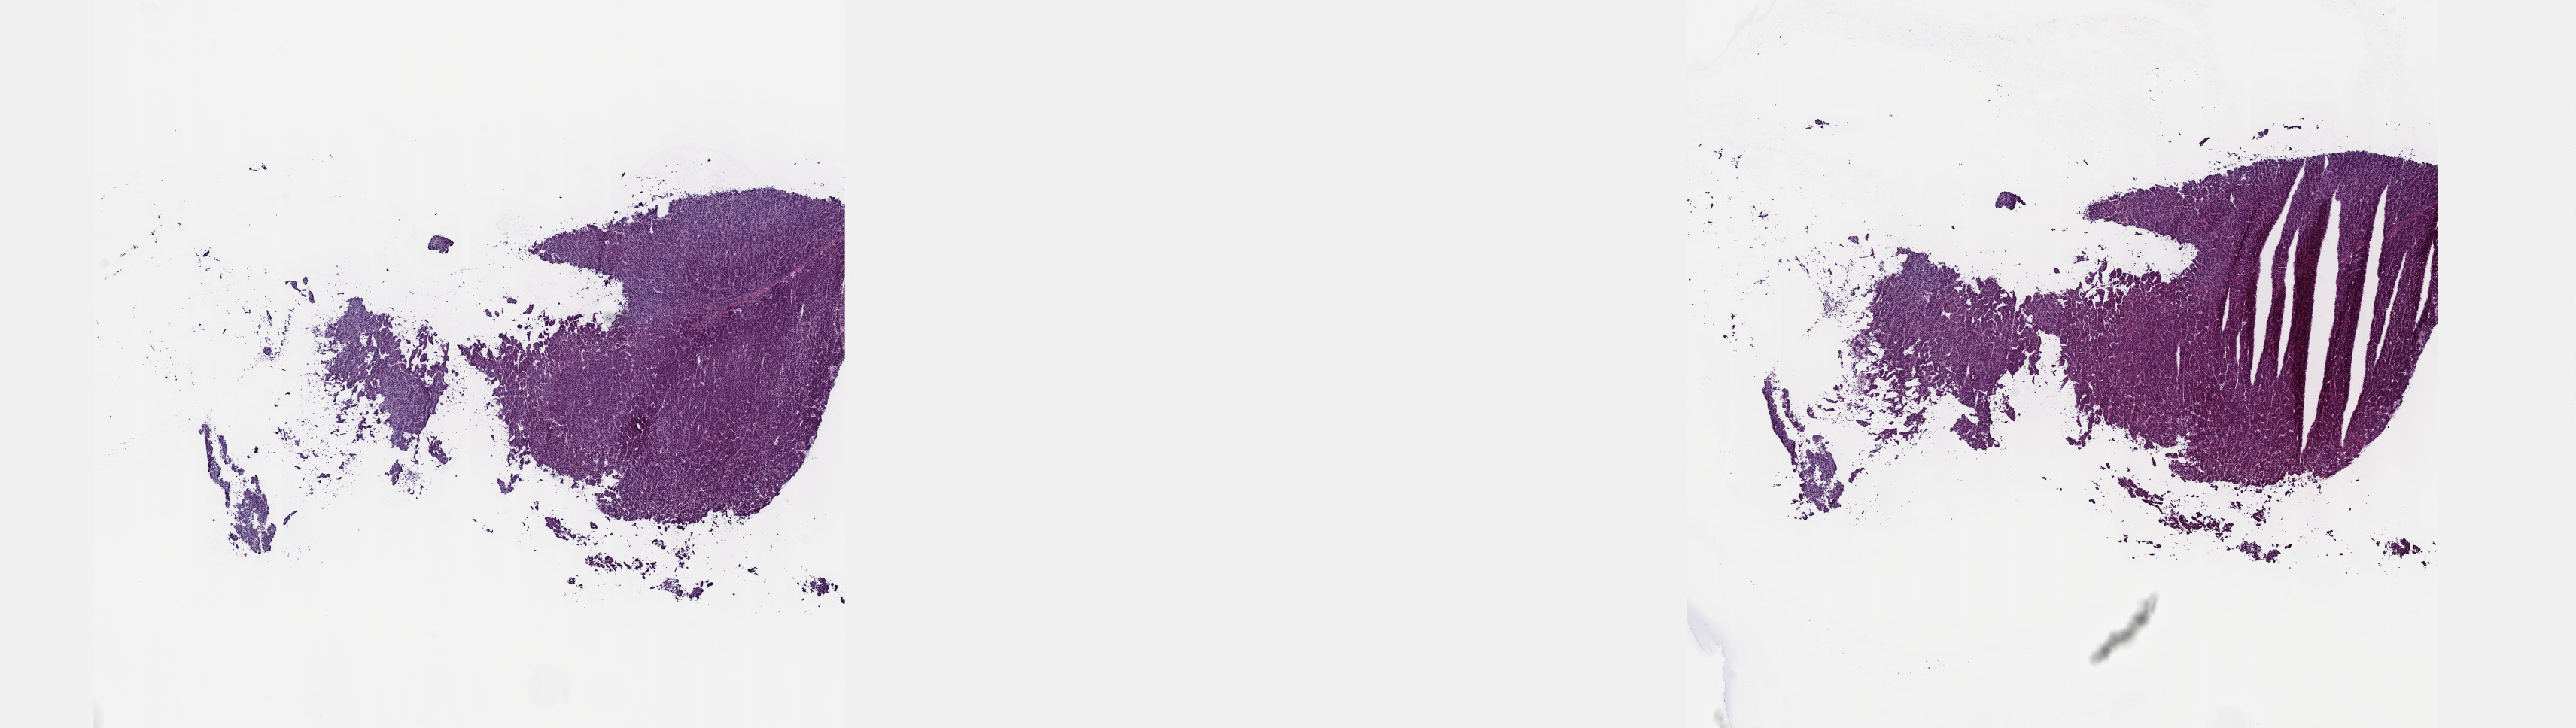
H&E whole-slide image, shown as a low-resolution overview of the whole scanned area (about 27.7 x 7.8 mm). Frozen section from the top of the tissue portion. Sample: primary tumour, liver. Male, age 74 years at initial diagnosis. Histologic grade: G1 (well differentiated). Slide review estimates, as recorded: tumour cells 80%, tumour nuclei 80%, normal cells 0%, stromal cells 20%, necrosis 0%. Inflammatory infiltration, as recorded: lymphocyte infiltration 3%, monocyte infiltration 1%, neutrophil infiltration 1%.
AJCC pathologic stage: I (7th edition). Histologic diagnosis: Hepatocellular carcinoma, NOS.